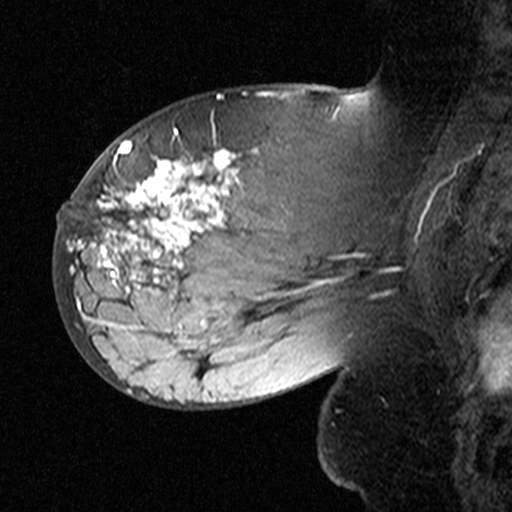
Breast MRI (dynamic contrast-enhanced), one sagittal slice. Position 22 of 44 along the scan axis. Dynamic contrast-enhanced study with each time point stored as its own series, time point 2 of 3 at this slice position (early post-contrast, ordered by acquisition time). 1.5 T. TE 4.5 ms, TR 11 ms. 512 × 512 image matrix, field of view 200 × 200 mm. Patient: female, 53 years. From the clinical record (not read from this slice): setting: breast cancer imaged before/during neoadjuvant chemotherapy; receptor status: HR-positive, HER2-negative.
Annotated regions visible in this slice (semi-automatic segmentation, software-assisted and operator-edited):
- analysis volume of interest (the breast-tissue region the enhancement analysis was run in; not a lesion): bounding box <76,140,311,353> (left, top, right, bottom; pixels)
- tumour enhancement mask (voxels above the 90 % enhancement threshold inside the analysis volume of interest): <76,147,259,324>